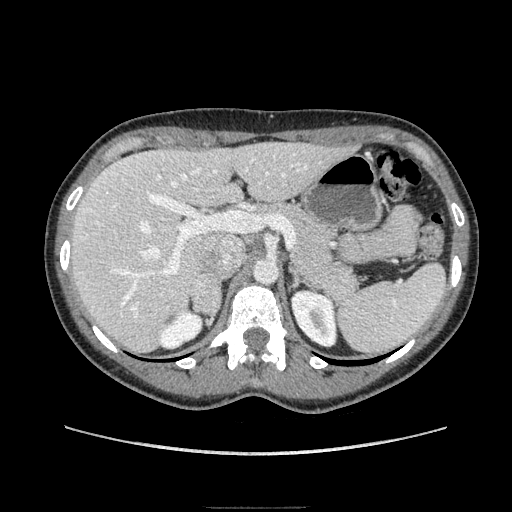
Contrast-enhanced abdominal CT, one axial slice; position 116 of 193 along the scan axis; soft-tissue window (W 400 / L 40 HU); 1.25 mm slice thickness; 512 × 512 image matrix, field of view 380 × 380 mm. Female patient. Case-level facts recorded for this patient, not image findings: diagnosis: adrenocortical carcinoma; tumour side: right adrenal.
Outlined on this slice (semi-automatically segmented with operator editing):
- mass: bounding box <194,275,220,318> (left, top, right, bottom; pixels)